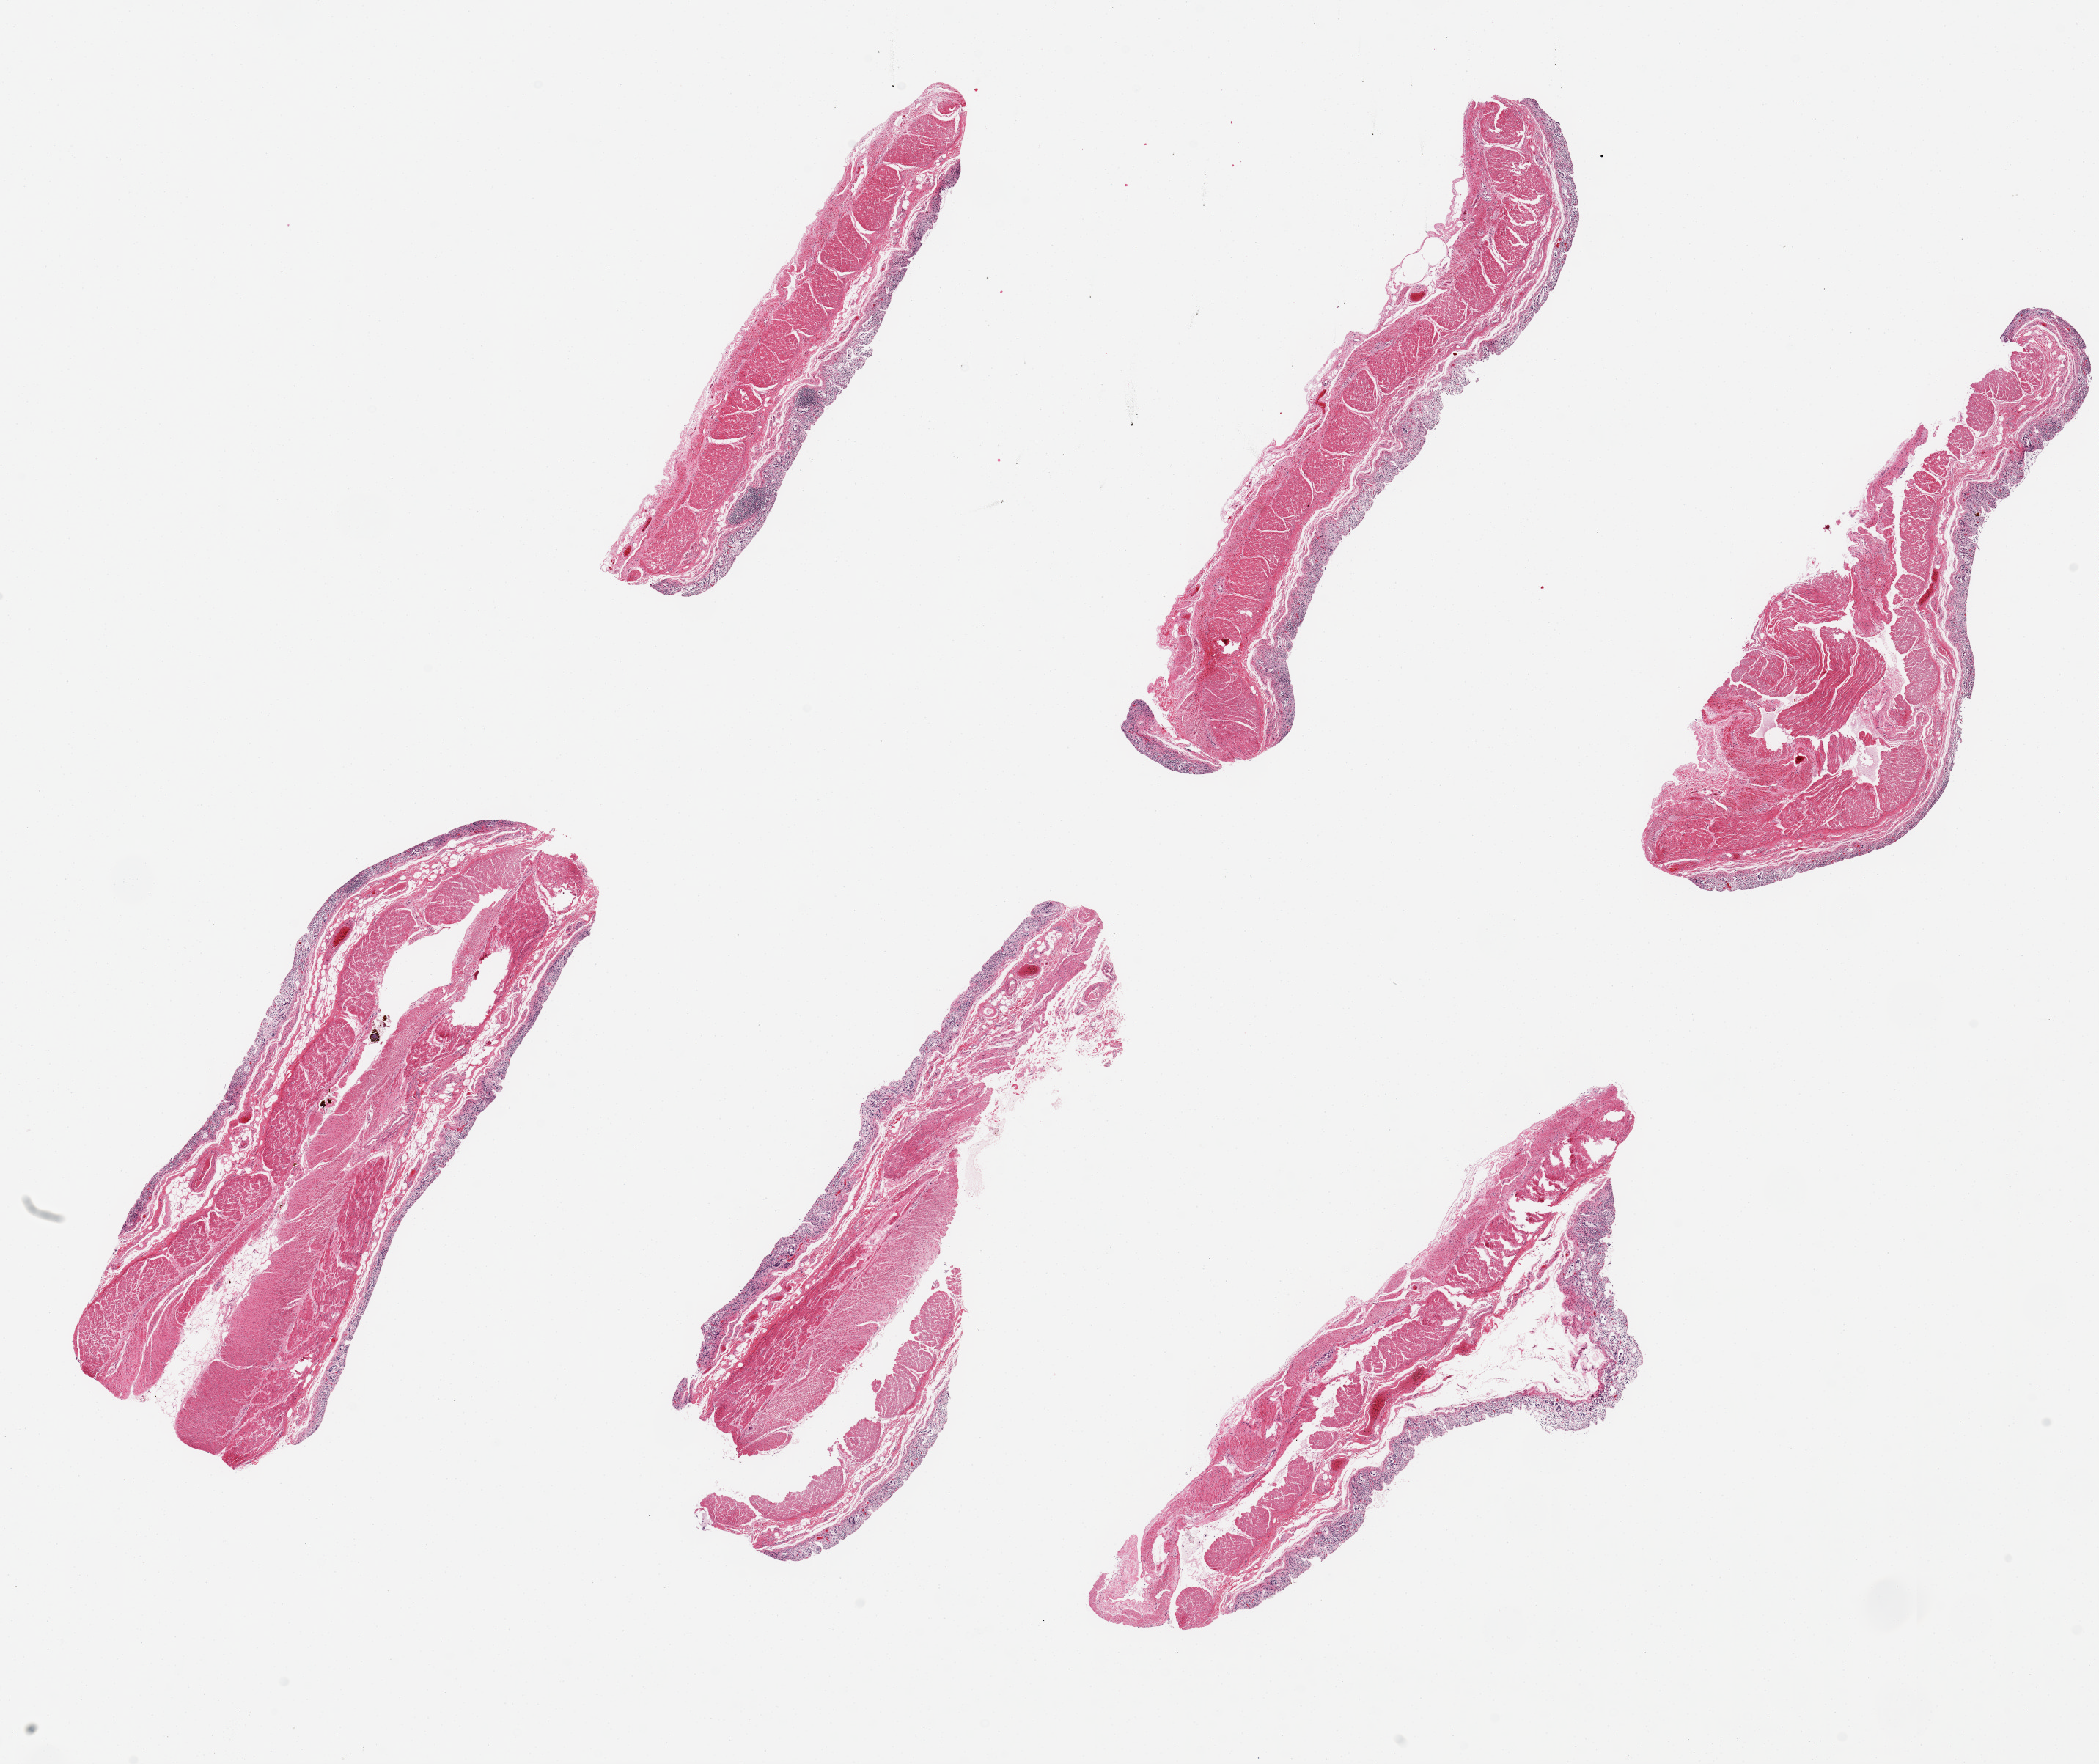
Hematoxylin and eosin (H&E) whole-slide image — a low-resolution overview of the entire scanned area, about 22.6 x 19.0 mm; PAXgene-fixed, paraffin-embedded tissue; target tissue: transverse colon; tissue donor sample. Donor: female.
Pathologist's review note for this sample: 6 pieces up to 8.3x2.6 mm; mucosa completely autolyzed; muscle moderately autolyzed.